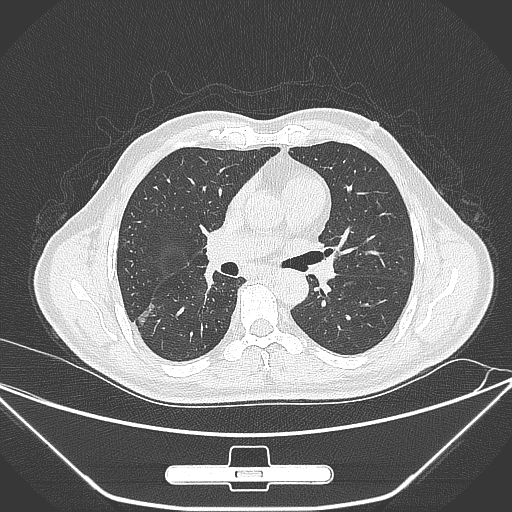
Chest CT, one axial slice; position 159 of 310 along the scan axis; lung window (W 1500 / L -600 HU); 512 × 512 image matrix, field of view 398 × 398 mm. Male patient, age 71 years. From the clinical record (not read from this slice): clinical TNM (as recorded): T1c N0 M0.
Outlined on this slice (rectangle marked by the reading radiologist):
- lung tumour (recorded histology: adenocarcinoma): bounding box <134,300,158,327> (left, top, right, bottom; pixels)